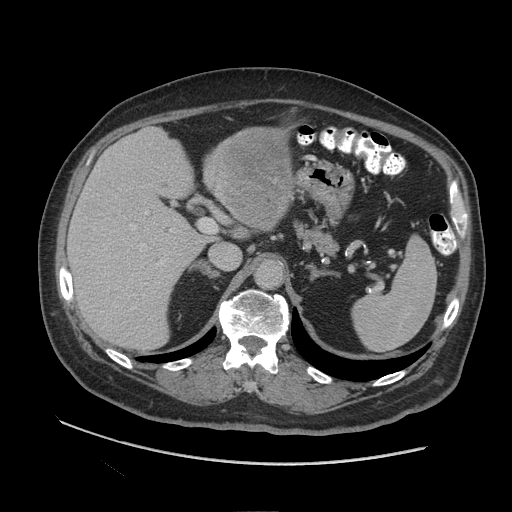
Contrast-enhanced abdominal CT (liver protocol), one axial slice; position 56 of 109 along the scan axis; 140 kVp; soft-tissue window (W 400 / L 40 HU); 2.5 mm slice thickness; 512 × 512 image matrix, field of view 420 × 420 mm. From the clinical record (not read from this slice): diagnosis: hepatocellular carcinoma (patient treated with transarterial chemoembolisation; whether this scan precedes or follows treatment is not stated here); TNM stage (as recorded): Stage-I; Child-Pugh class: A.
Annotated regions visible in this slice (semi-automatically segmented with operator editing):
- liver parenchyma outside the tumour (the mass and vessels are separate outlines, so this box may not span the whole liver): box from (x=68, y=128) to (x=250, y=350) px
- mass: (x=208, y=126)–(x=292, y=231)
- liver vessels: (x=130, y=212)–(x=172, y=265)